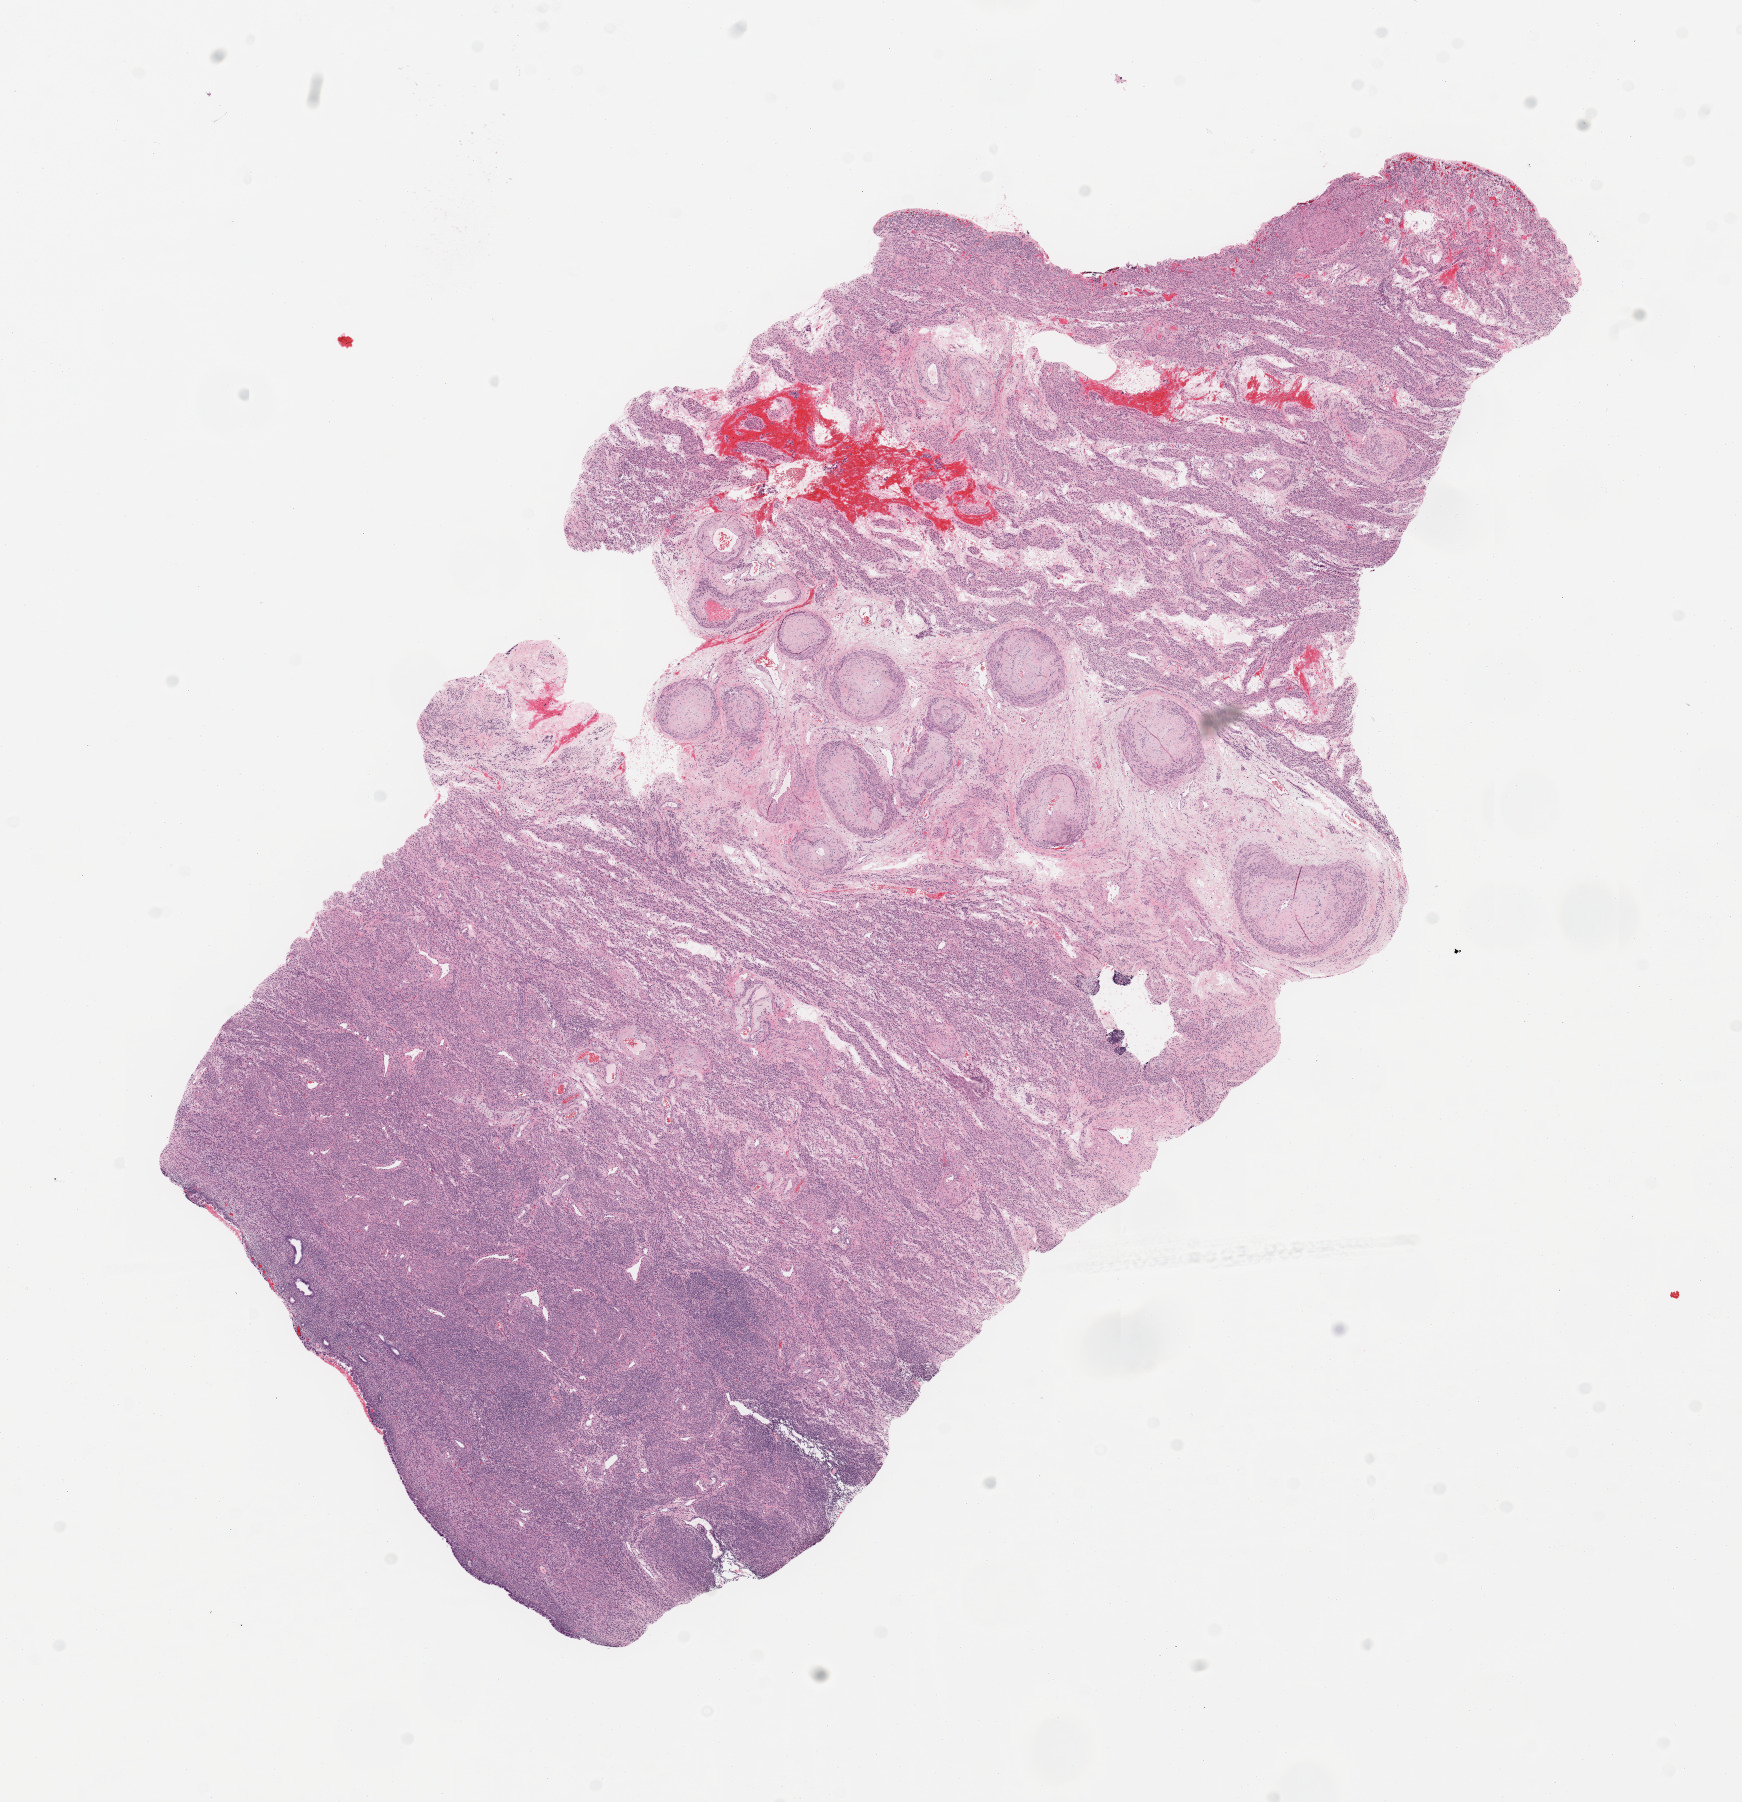
H&E-stained whole-slide image, a low-resolution overview of the entire scanned area, about 13.8 x 14.3 mm; uterus, normal (non-tumour) tissue. Female, 63 y/o.
• this section: normal (non-tumour) tissue from the same patient
• patient diagnosis: Endometrioid adenocarcinoma, NOS